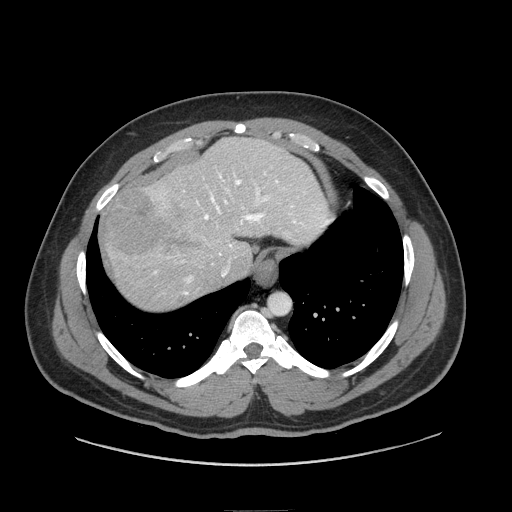
Contrast-enhanced abdominal CT (liver protocol), one axial slice. Slice 65 of 87 in the series (ordered by position). Reconstruction kernel STANDARD. 140 kVp. Soft-tissue window (W 400 / L 40 HU). 512 × 512 image matrix, field of view 440 × 440 mm. Case-level facts recorded for this patient, not image findings: diagnosis: hepatocellular carcinoma (patient treated with transarterial chemoembolisation; whether this scan precedes or follows treatment is not stated here); TNM stage (as recorded): Stage-II; Child-Pugh class: A; tumour differentiation: moderately differentiated; tumour nodularity: uninodular.
Structures marked on this image (semi-automatic segmentation, software-assisted and operator-edited):
- liver parenchyma outside the tumour (the mass and vessels are separate outlines, so this box may not span the whole liver): bounding box <104,138,330,310> (left, top, right, bottom; pixels)
- mass: <102,183,193,262>
- liver vessels: <154,172,329,295>